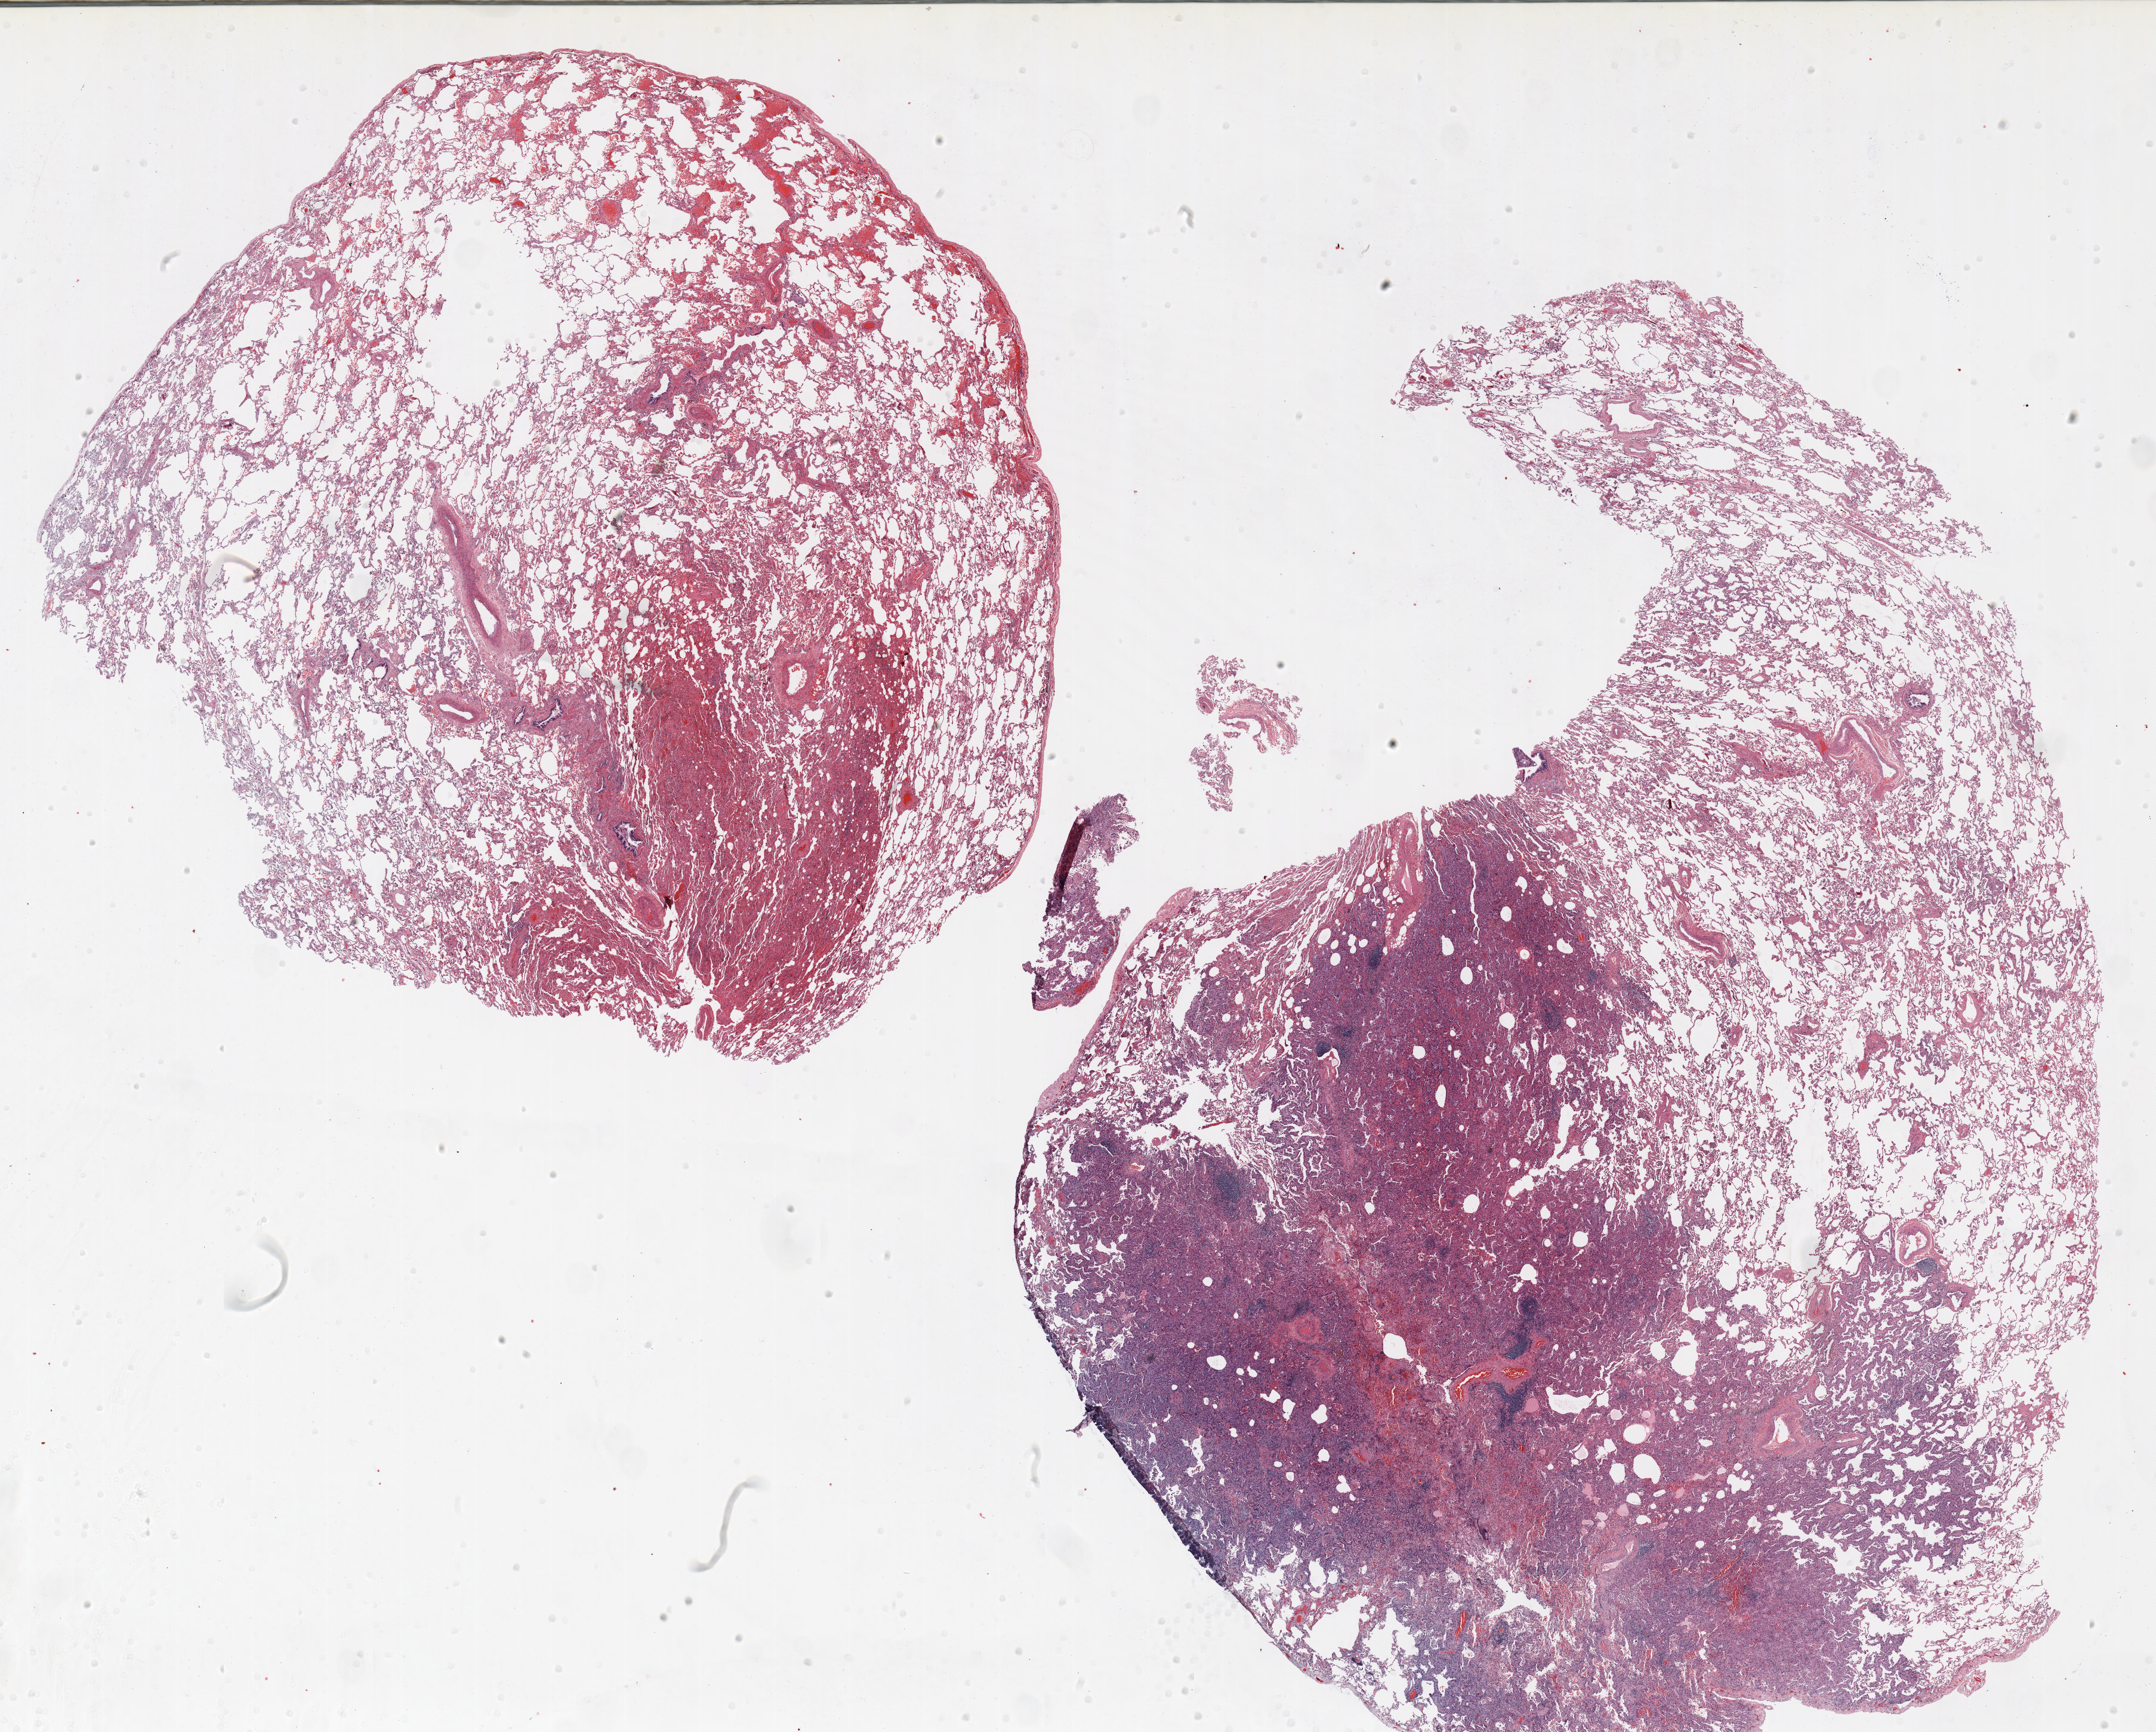
Whole-slide histology image, Hematoxylin and eosin (H&E) stained, a low-resolution overview of the entire scanned area, about 29.0 x 23.3 mm; FFPE section; lung tissue. Female patient, aged 56 at enrolment. Current smoker at enrolment. Grade: well differentiated (G1).
Primary tumour location (clinical record): right upper lobe. Tumour size (pathology): 15 mm. Stage (AJCC 6th edition): IA. ICD-O-3 topography: upper lobe of lung (C34.1). Participant's lung-cancer diagnosis: Bronchiolo-alveolar adenocarcinoma, NOS.